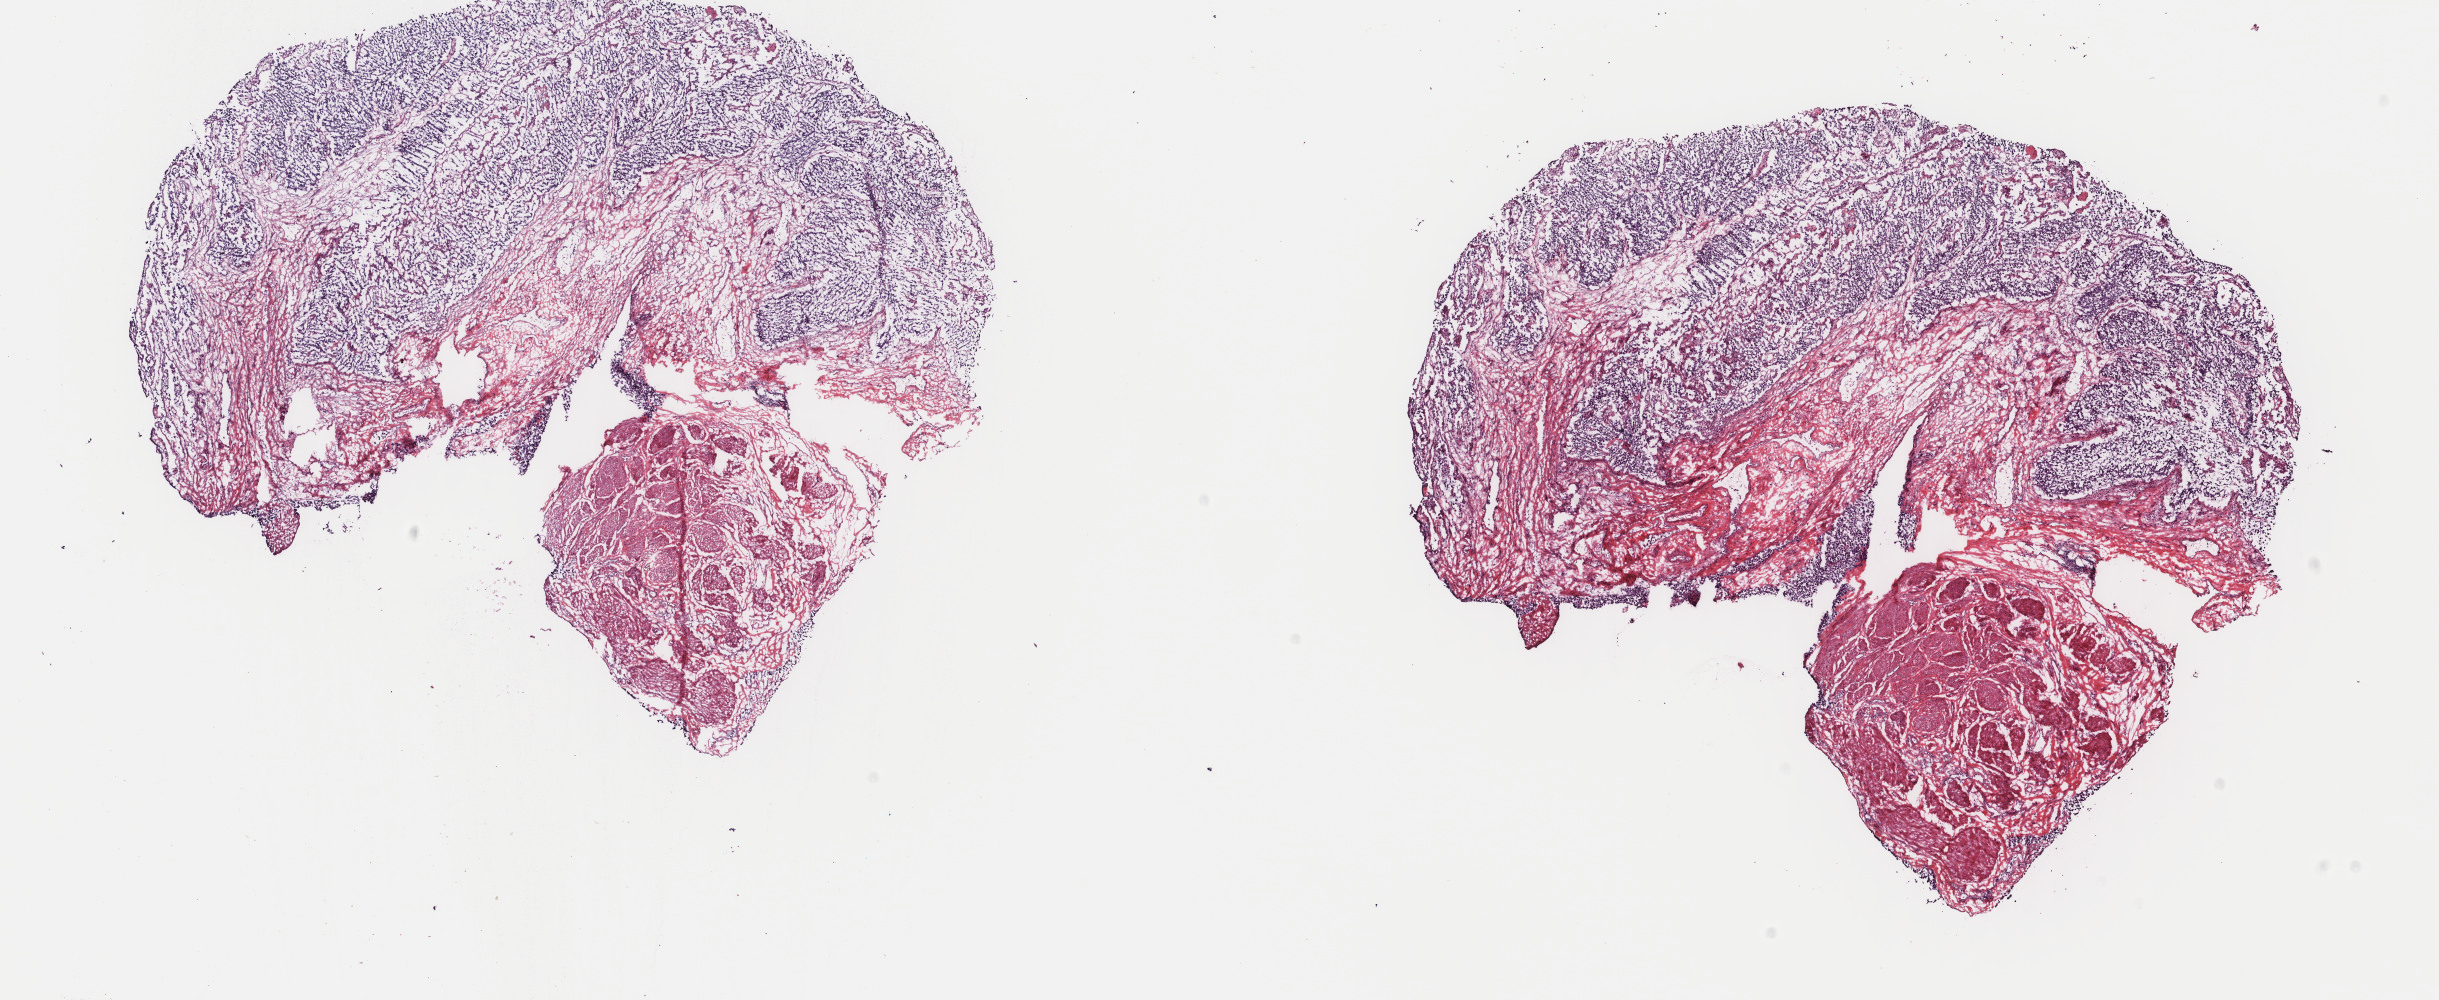
Digitized H&E-stained tissue section (whole slide) — whole scanned area (about 19.4 x 7.9 mm, acquisition: 40x scan) shown as a low-resolution overview. Frozen section from the top of the tissue portion. Bladder, primary tumour sample. Male patient; age at initial diagnosis 81 years. Histologic grade: high grade. Pathologist review of this section (percent, as recorded): tumour cells 50%, tumour nuclei 60%, normal cells 0%, stromal cells 50%, necrosis 0%. Inflammatory infiltration, as recorded: lymphocyte infiltration 0%, monocyte infiltration 0%, neutrophil infiltration 0%.
AJCC pathologic stage: IV (7th edition). Pathologic diagnosis: Transitional cell carcinoma.